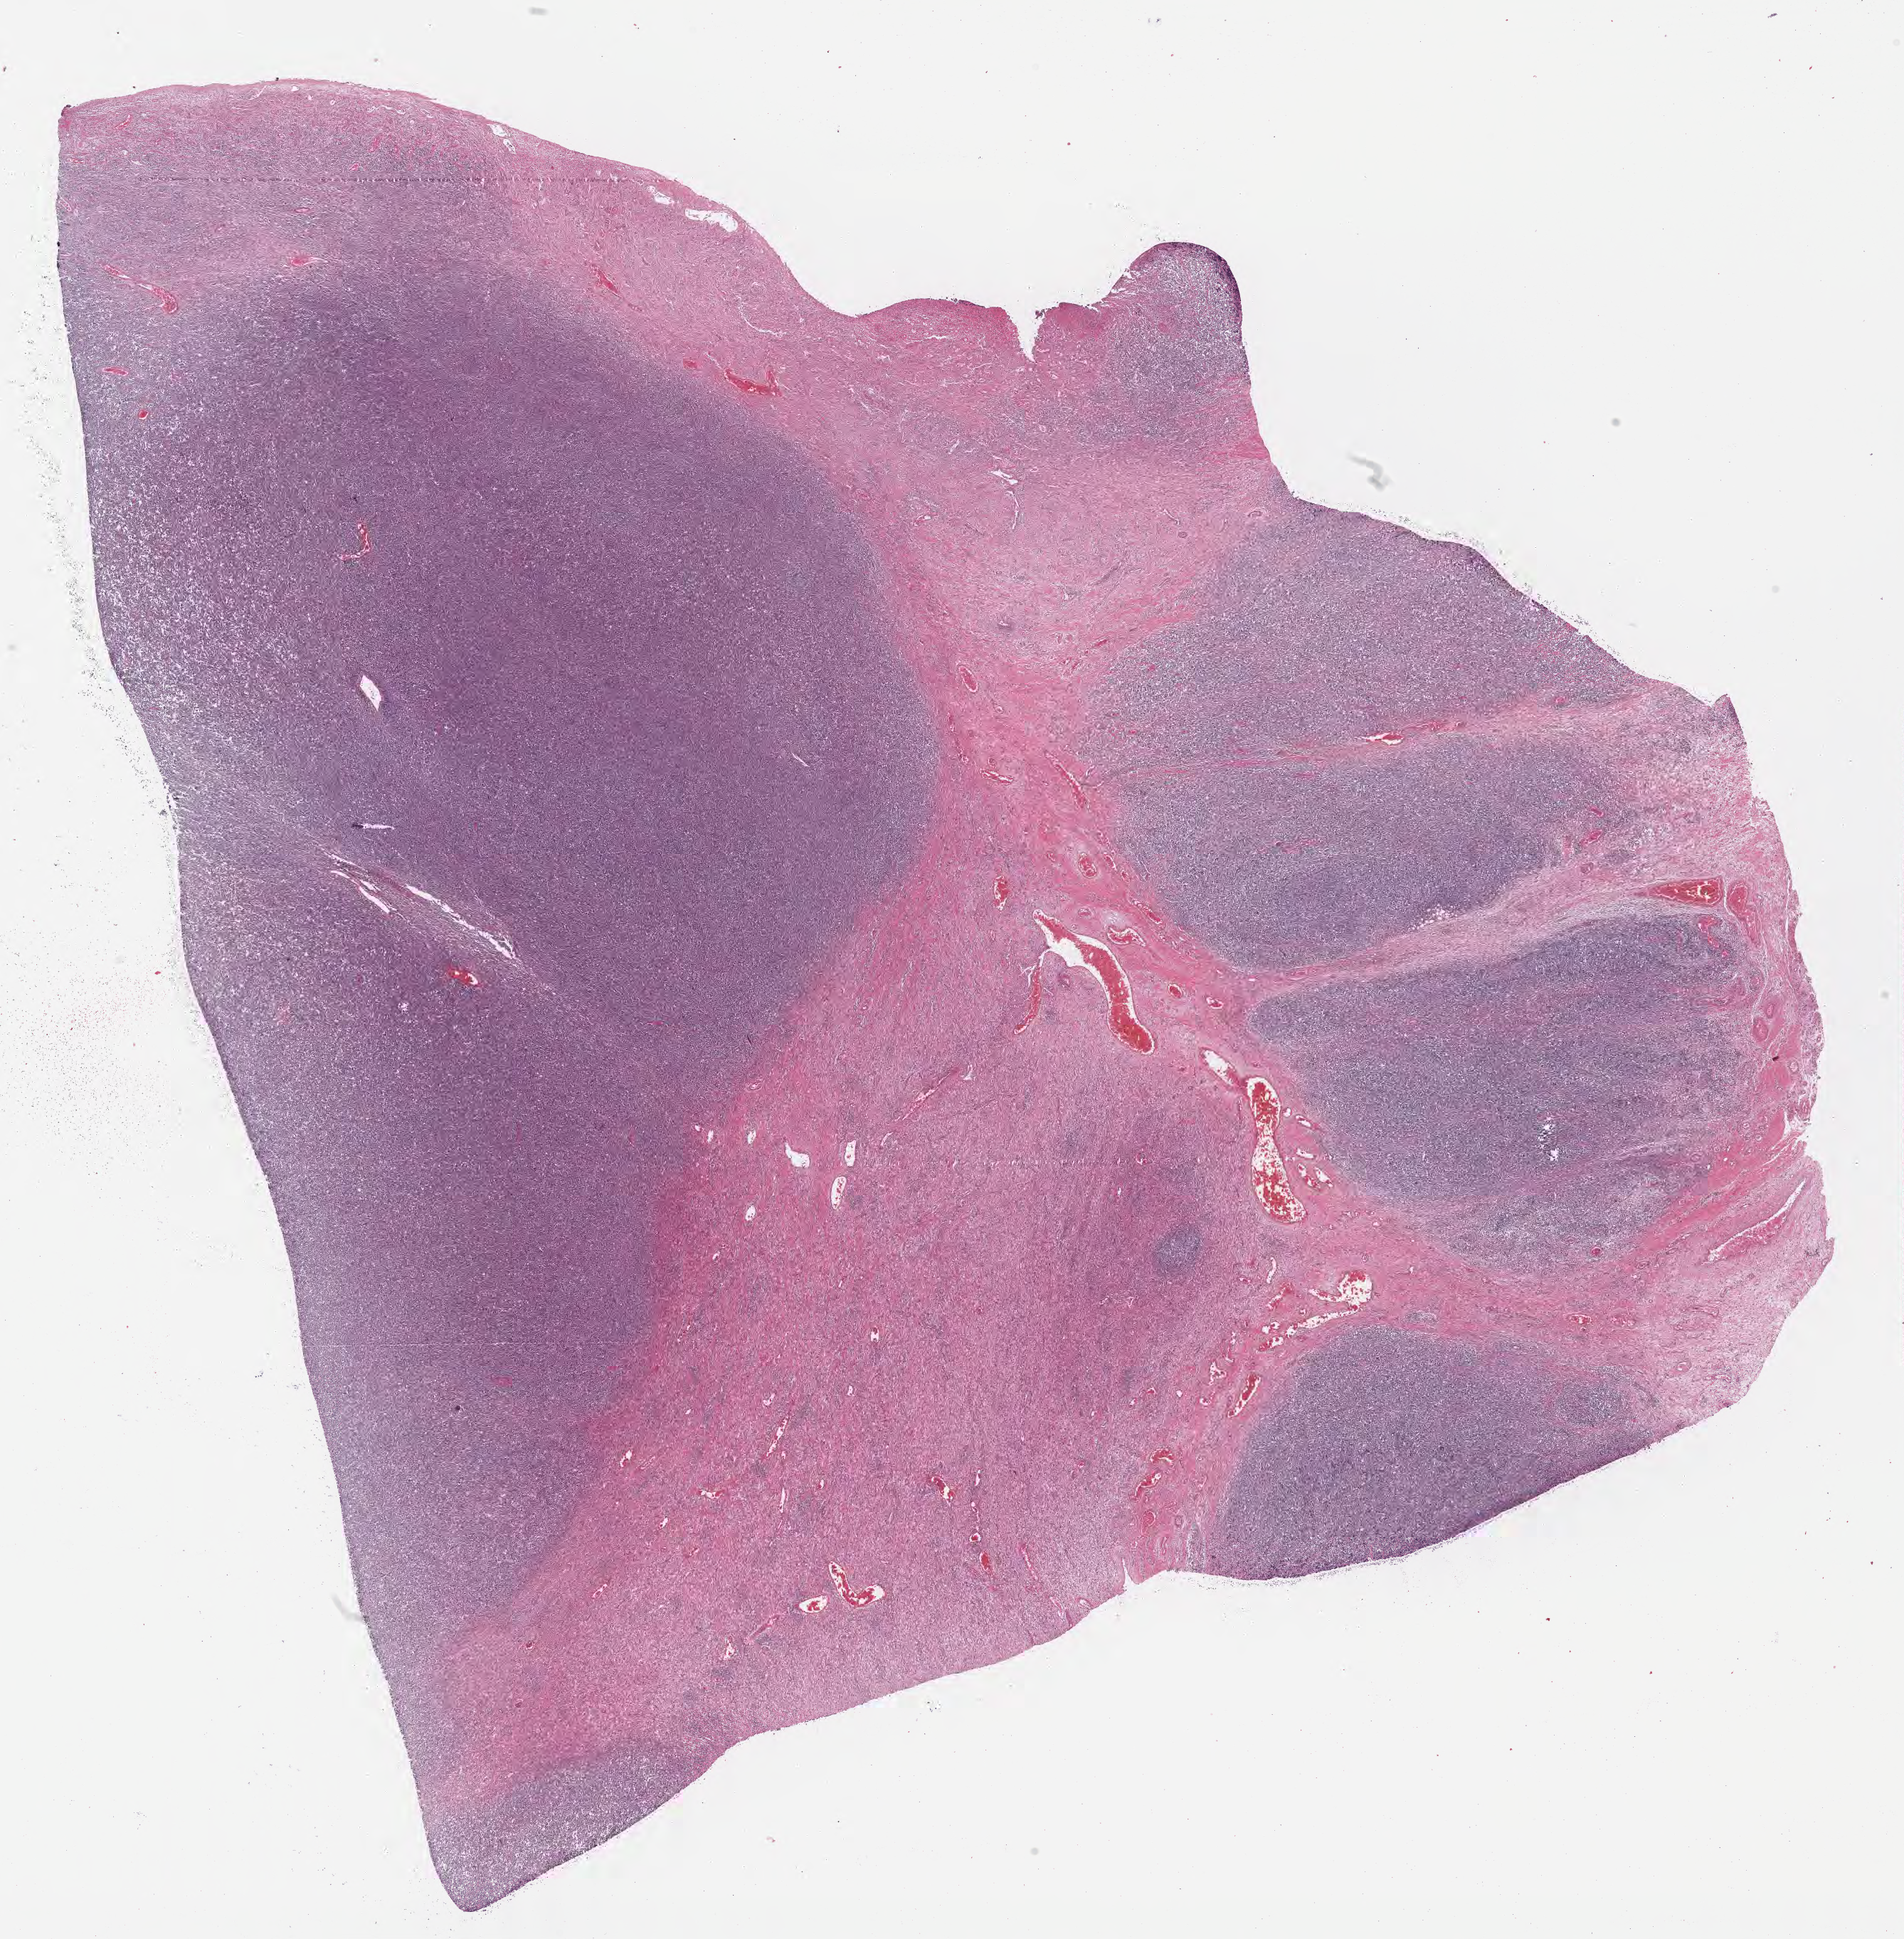
Whole-slide image, H&E stain — a low-resolution overview of the entire scanned area, about 21.6 x 22.0 mm, tumor tissue. Female, age 8 years at initial diagnosis.
* diagnosis: Burkitt lymphoma, NOS